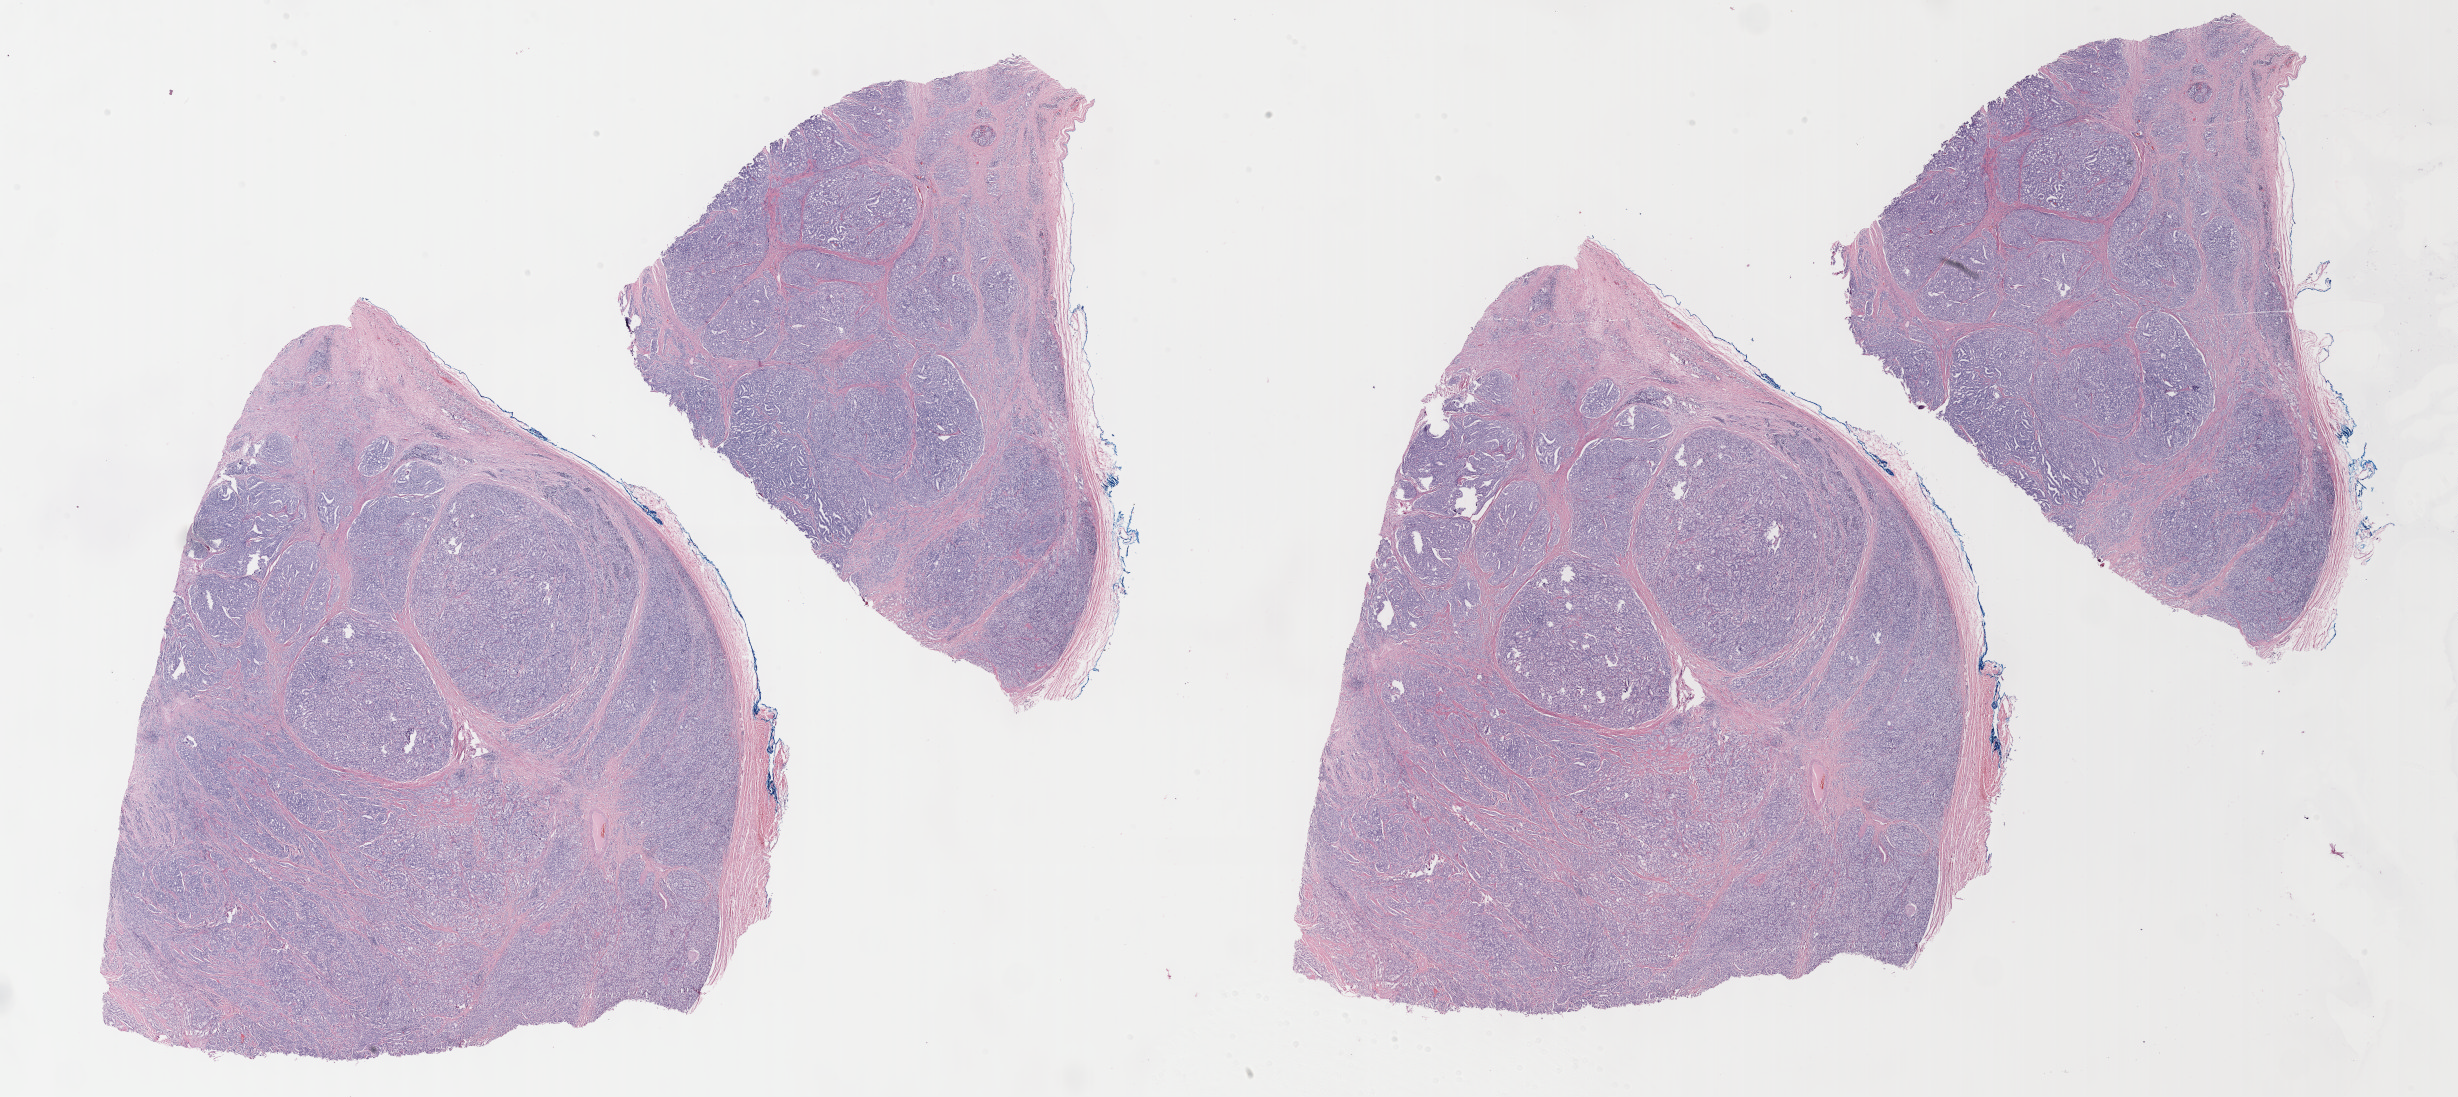
Whole-slide histology image, H&E — low-resolution overview of the scanned area, about 39.8 x 17.7 mm (from a 40x scan); formalin-fixed paraffin-embedded (FFPE) diagnostic section; primary tumour sample from the prostate. Male, age 70 years at initial diagnosis. Gleason score: 8 (4+4).
Laterality: bilateral. Pathologic diagnosis: Adenocarcinoma, NOS.